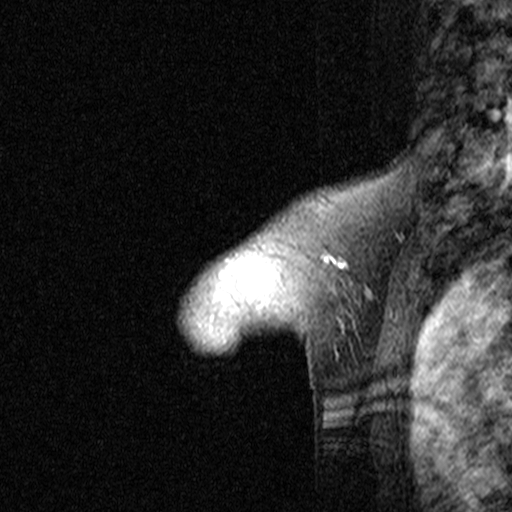
Breast MRI (dynamic contrast-enhanced), one sagittal slice. Position 35 of 44 along the scan axis. Dynamic contrast-enhanced study with each time point stored as its own series, time point 2 of 3 at this slice position (early post-contrast, ordered by acquisition time). 1.5 T. TE 4.5 ms, TR 11 ms. 512 × 512 image matrix, field of view 200 × 200 mm. Patient: female, 46 years. From the clinical record (not read from this slice): setting: breast cancer imaged before/during neoadjuvant chemotherapy; receptor status: HER2-positive.
Outlined on this slice (semi-automatically segmented with operator editing):
- analysis volume of interest (the breast-tissue region the enhancement analysis was run in; not a lesion): bounding box (x1, y1, x2, y2) in pixels: (165, 172, 359, 393)
- tumour enhancement mask (voxels above the 90 % enhancement threshold inside the analysis volume of interest): (324, 259, 347, 268)